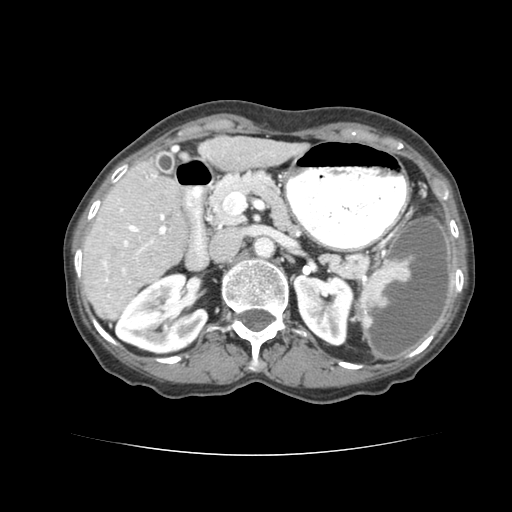
Contrast-enhanced abdominal CT (liver protocol), one axial slice; position 36 of 77 along the scan axis; reconstruction kernel STANDARD; soft-tissue window (W 400 / L 40 HU); 2.5 mm slice thickness; 512 × 512 image matrix. Case-level facts recorded for this patient, not image findings: diagnosis: hepatocellular carcinoma (patient treated with transarterial chemoembolisation; whether this scan precedes or follows treatment is not stated here); TNM stage (as recorded): Stage-I; Child-Pugh class: A; tumour differentiation: well differentiated; tumour nodularity: uninodular.
Outlined on this slice (semi-automatically segmented with operator editing):
- liver parenchyma outside the tumour (the mass and vessels are separate outlines, so this box may not span the whole liver): bounding box [x1, y1, x2, y2] px = [80, 136, 309, 318]
- liver vessels: [103, 153, 241, 289]